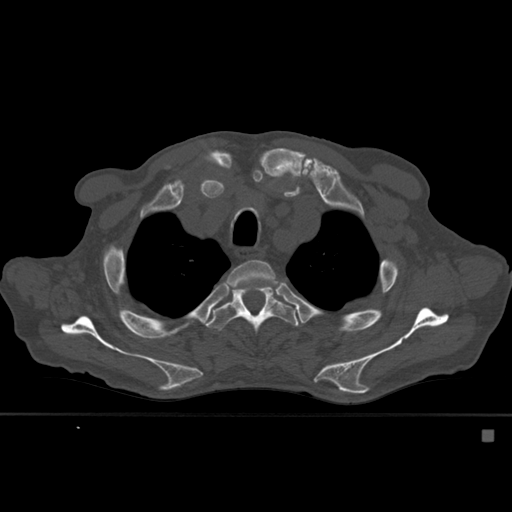
CT including the spine, one axial slice; slice 422 of 527 in the series (ordered by position); bone window (W 1800 / L 400 HU); 512 × 512 image matrix, field of view 373 × 373 mm. Male patient, age 78 years. Case-level facts recorded for this patient, not image findings: primary cancer: prostate.
Annotated regions visible in this slice (semi-automatic segmentation, software-assisted and operator-edited):
- T3 vertebra: box from (x=225, y=260) to (x=279, y=290) px
- T4 vertebra: (x=206, y=285)–(x=300, y=335)